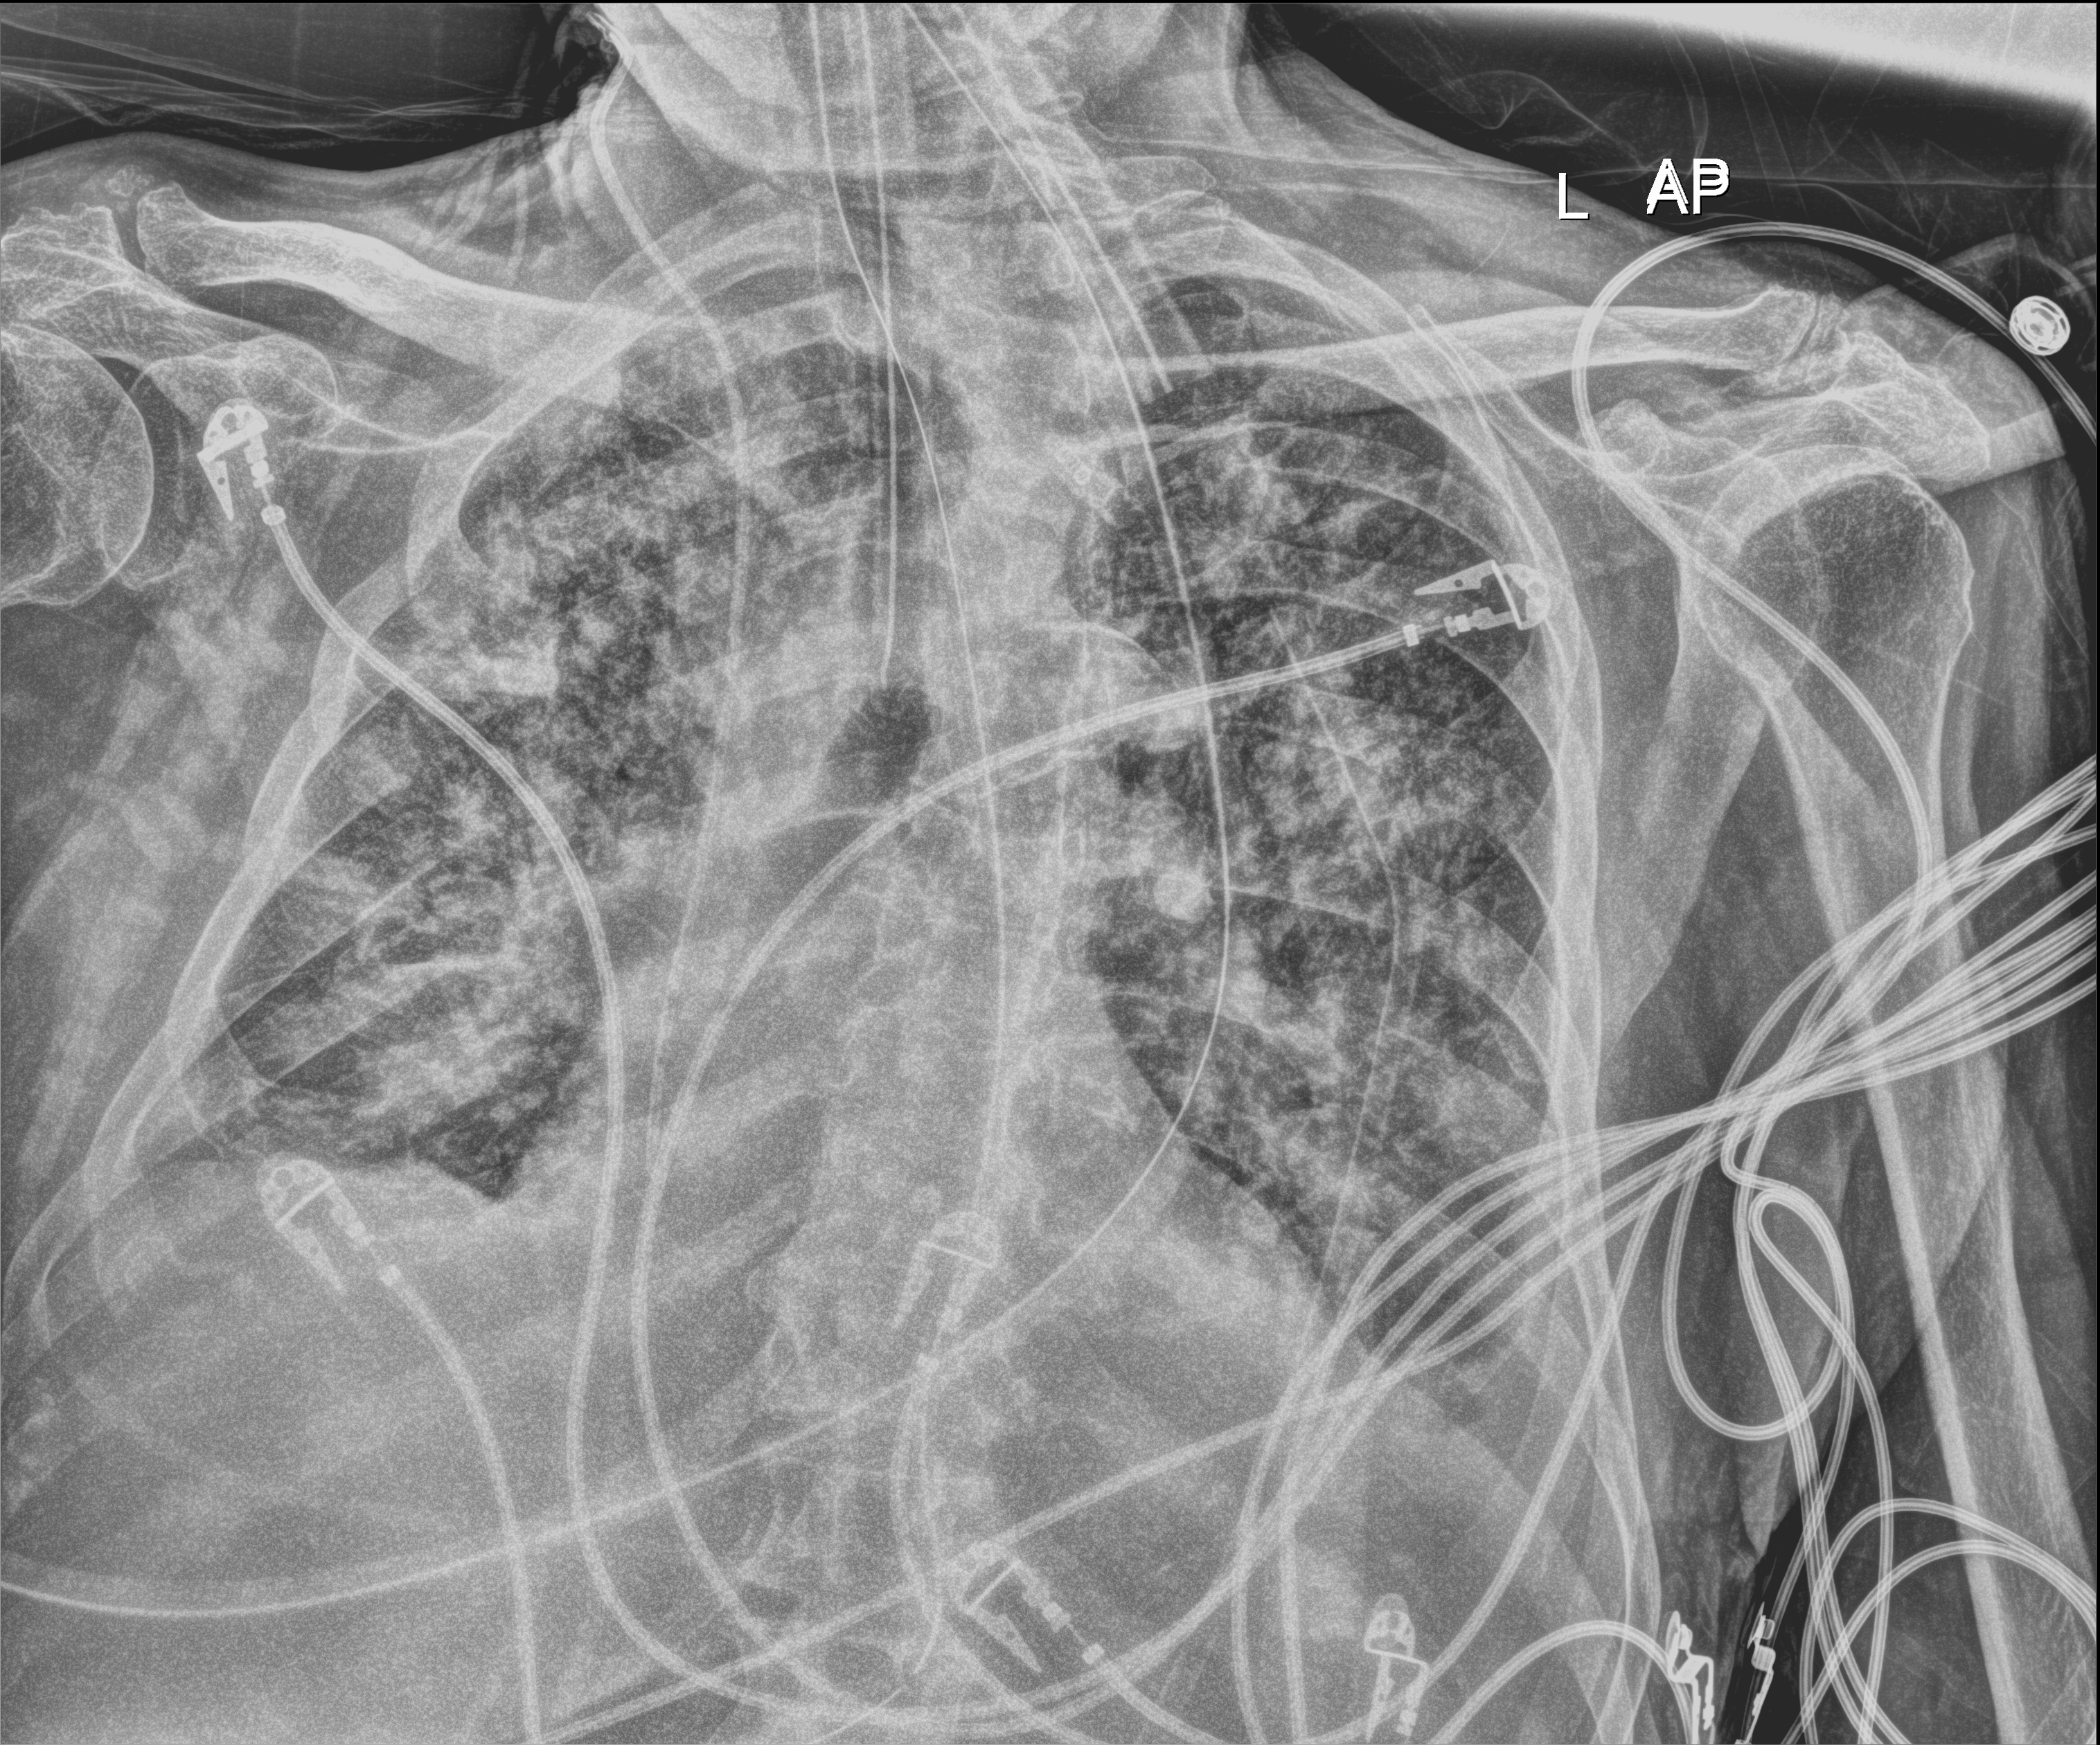
Portable chest radiograph. Patient hospitalised with COVID-19; male, aged 75–90 years.
Hospital-stay facts (about this admission, not read from this image; timing relative to this image not recorded): admitted to intensive care during this hospital stay: yes; mechanically ventilated during this hospital stay: yes.